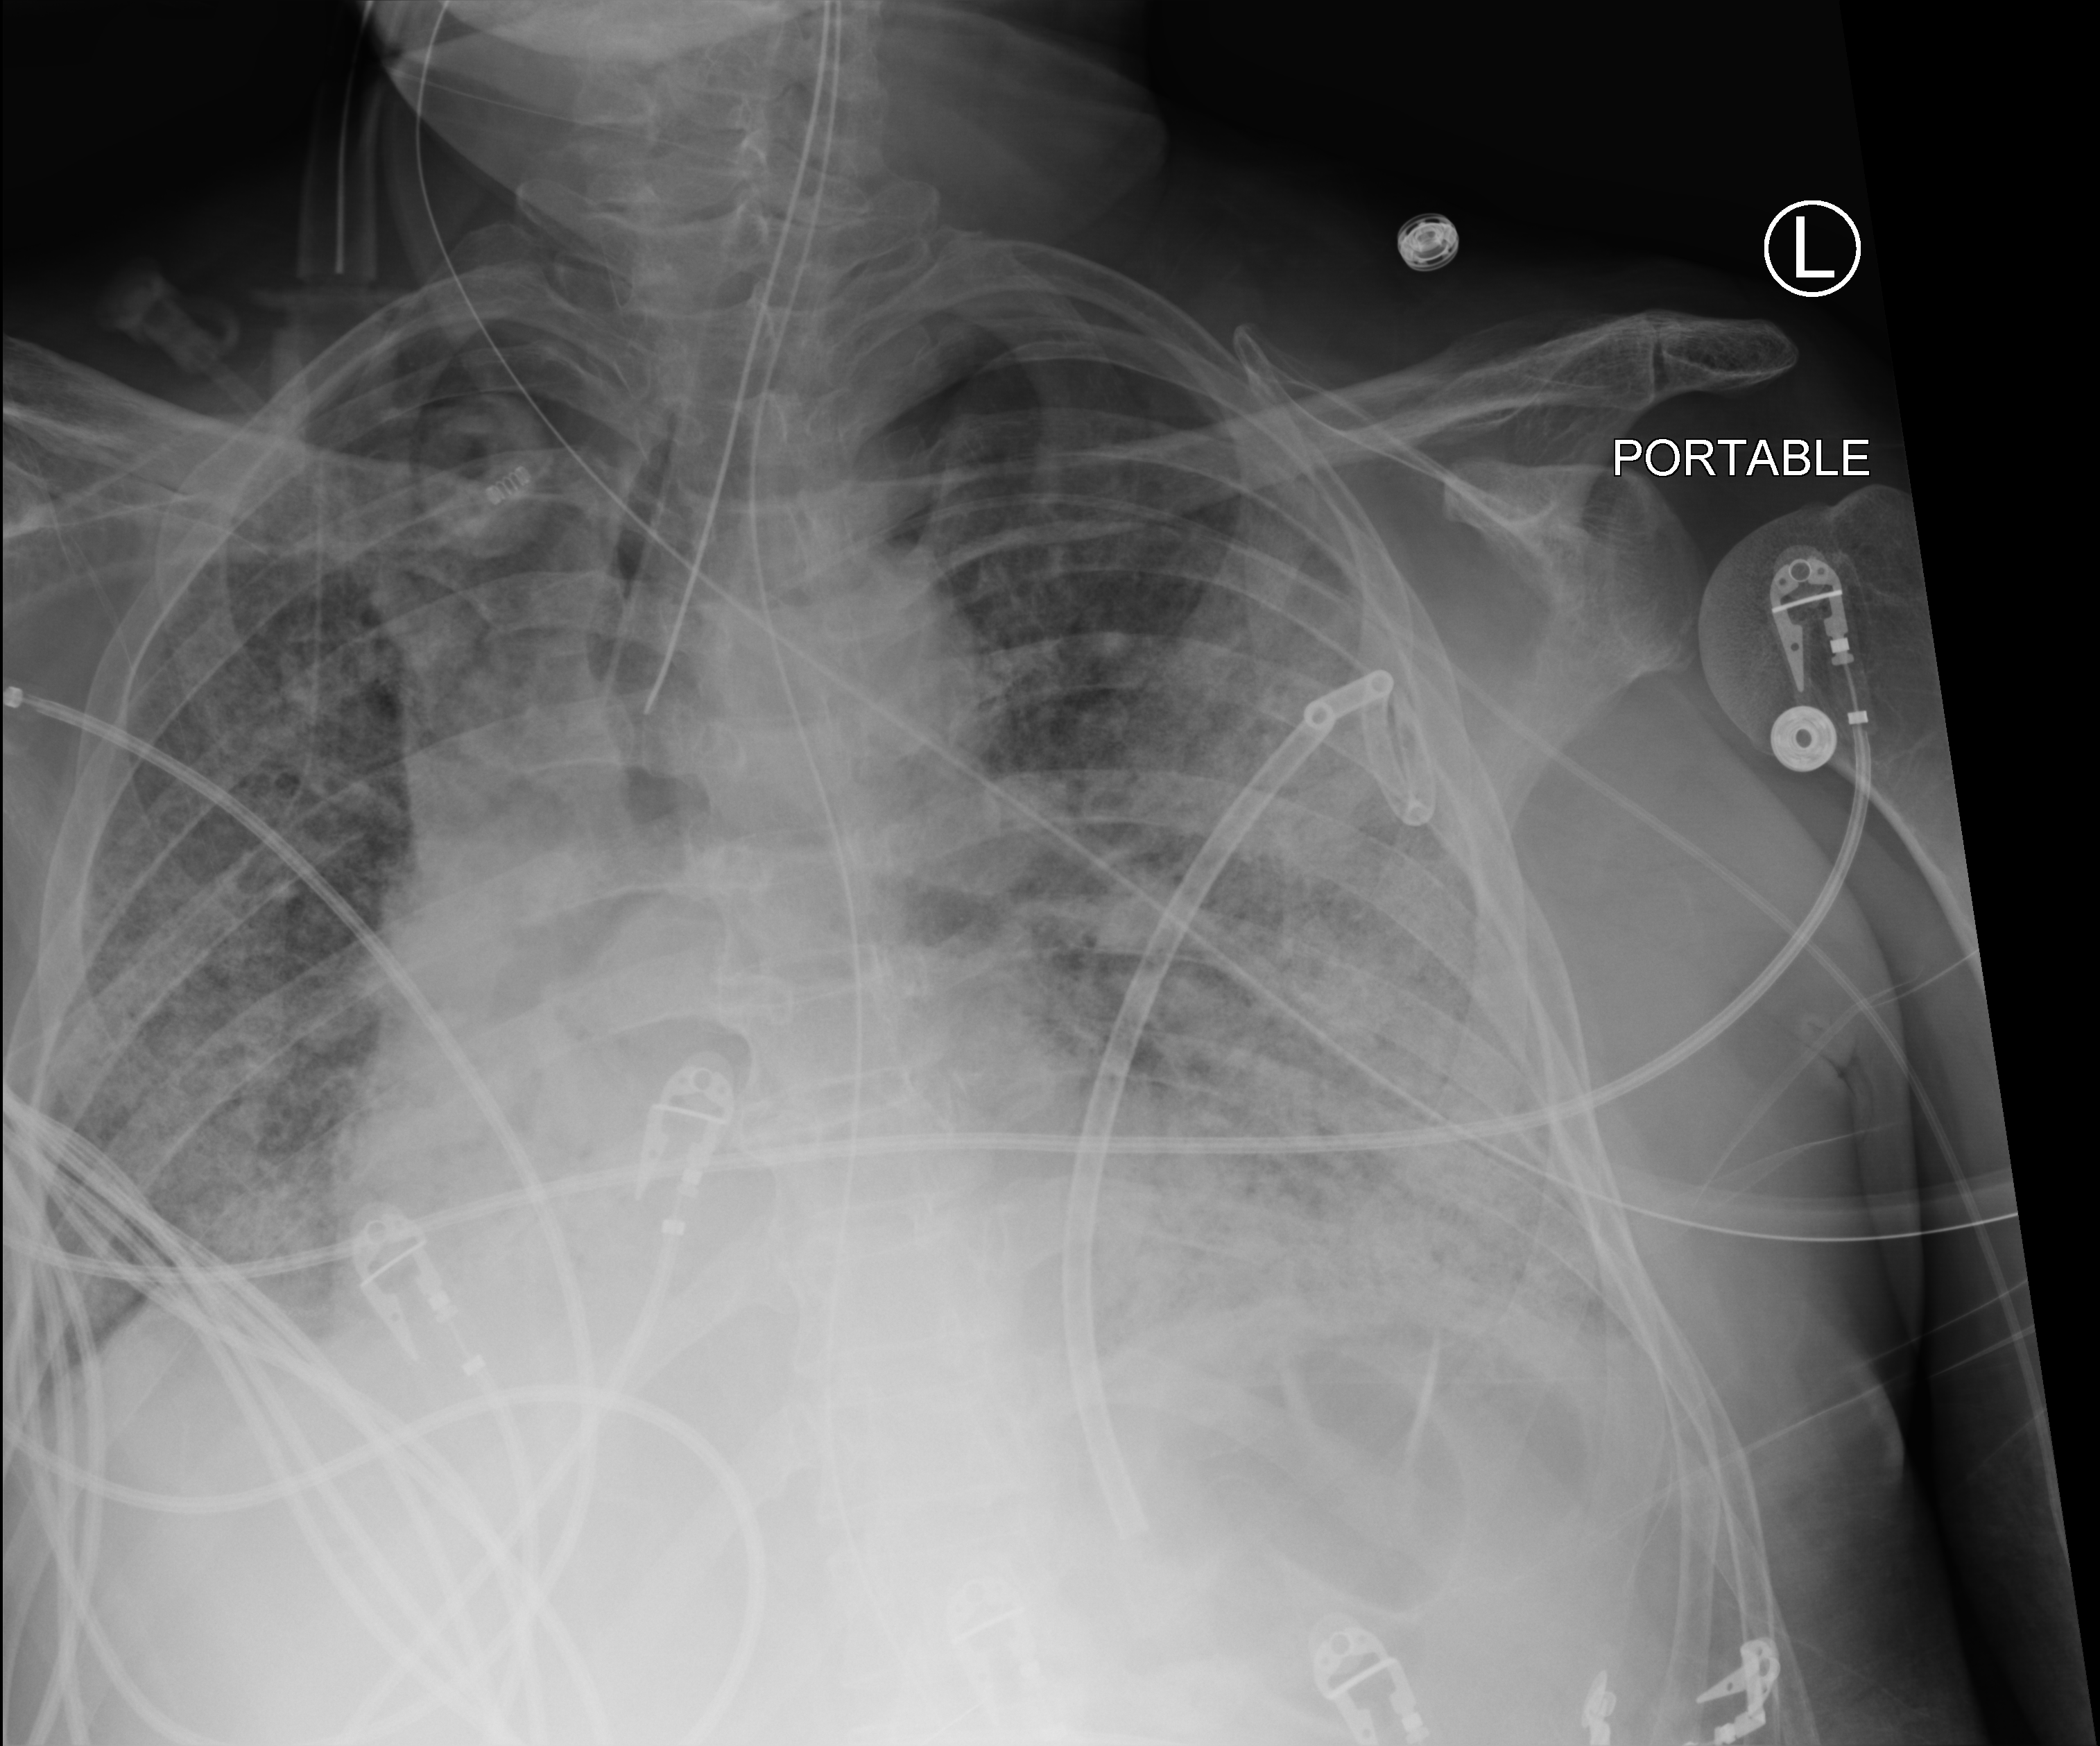
Portable chest radiograph; anteroposterior (AP) projection. Patient hospitalised with COVID-19; male, aged 60–74 years.
Admission-level facts for this patient (not findings on this image; timing relative to this image not recorded): admitted to intensive care during this hospital stay: yes.